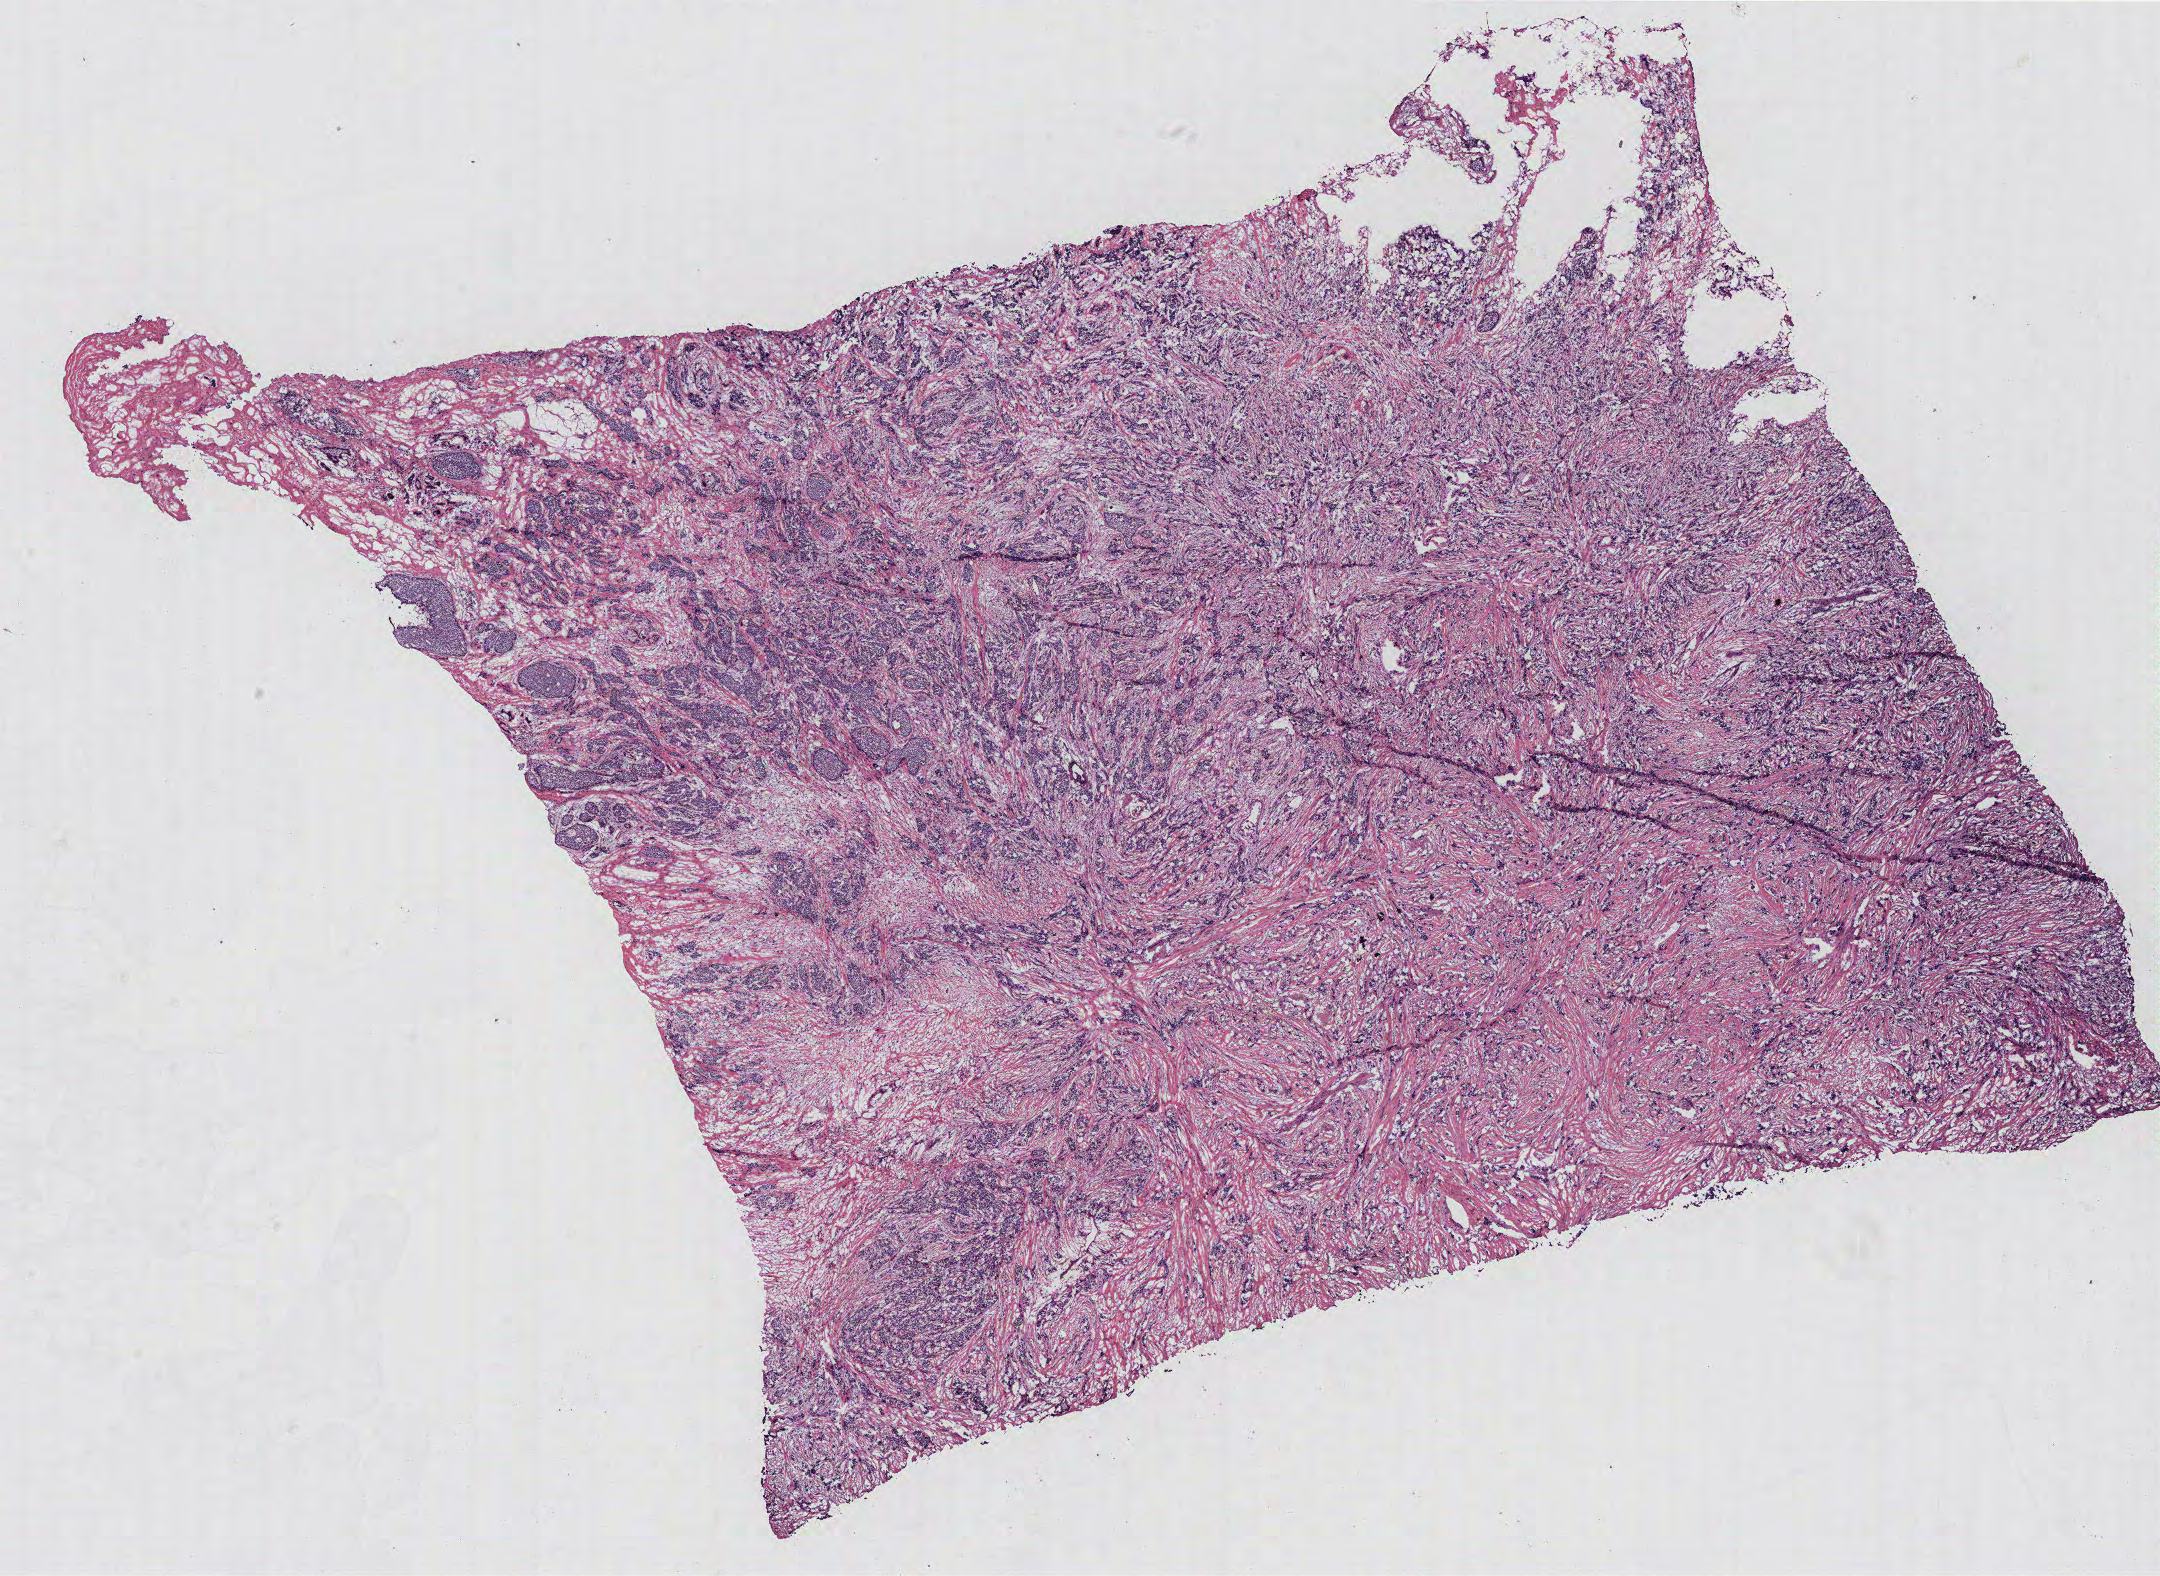
Whole-slide histology image, H&E-stained, a low-resolution overview of the entire scanned area, about 17.3 x 12.6 mm. Breast, tumour tissue. 47-year-old female patient.
Histologic diagnosis: Infiltrating duct carcinoma, NOS. AJCC pathologic stage: IIIC.